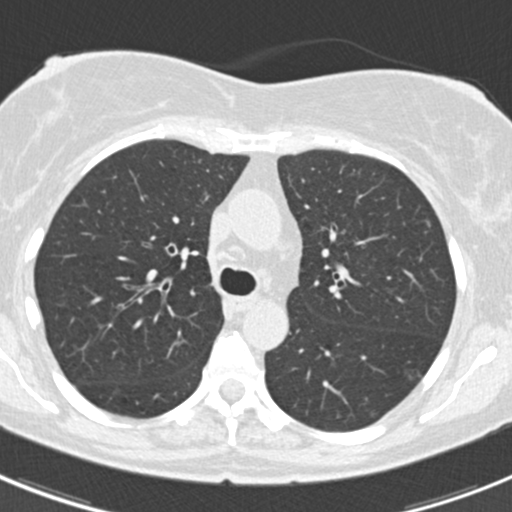
Chest CT (low-dose screening protocol), one axial image. Baseline screening round. Lung window (W 1500 / L -600 HU). Standard (soft-tissue) reconstruction kernel (B30f). Female participant, aged 60 years at enrolment. Current smoker at enrolment.
Expert reader's lesion annotation, box from (x=418, y=215) to (x=442, y=238) px. The screening reader recorded 3 non-calcified nodules or masses ≥4 mm on this exam (lingula, left lower lobe, lingula); which of them this box marks is not recorded. Official screen result: positive, change unspecified: nodule(s) >= 4 mm or enlarging nodule(s), mass(es), or other non-specific abnormalities suspicious for lung cancer. Later outcome: lung cancer diagnosed 886 days after this screen (after the third annual screen) — non-small cell carcinoma, left upper lobe, poorly differentiated (G3), stage IB (AJCC 6th edition), 7 mm at pathology.